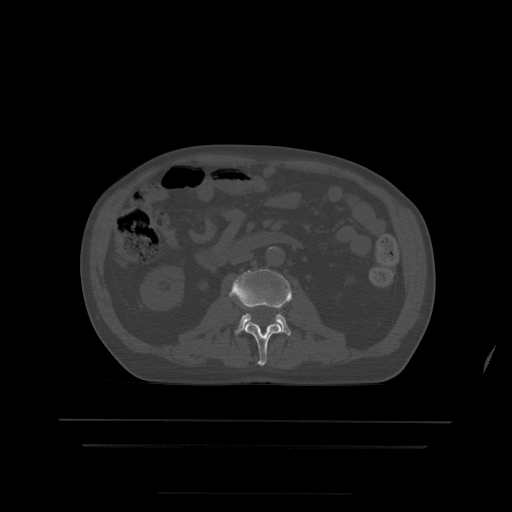
CT including the spine, one axial slice; position 133 of 522 along the scan axis; bone window (W 1800 / L 400 HU); 1.25 mm slice thickness; 512 × 512 image matrix, field of view 436 × 436 mm. Patient age 68 years. From the clinical record (not read from this slice): primary cancer: urothelial.
Structures marked on this image (semi-automatically segmented with operator editing):
- L2 vertebra: bounding box [x1, y1, x2, y2] px = [245, 322, 281, 366]
- L3 vertebra: [230, 269, 293, 336]